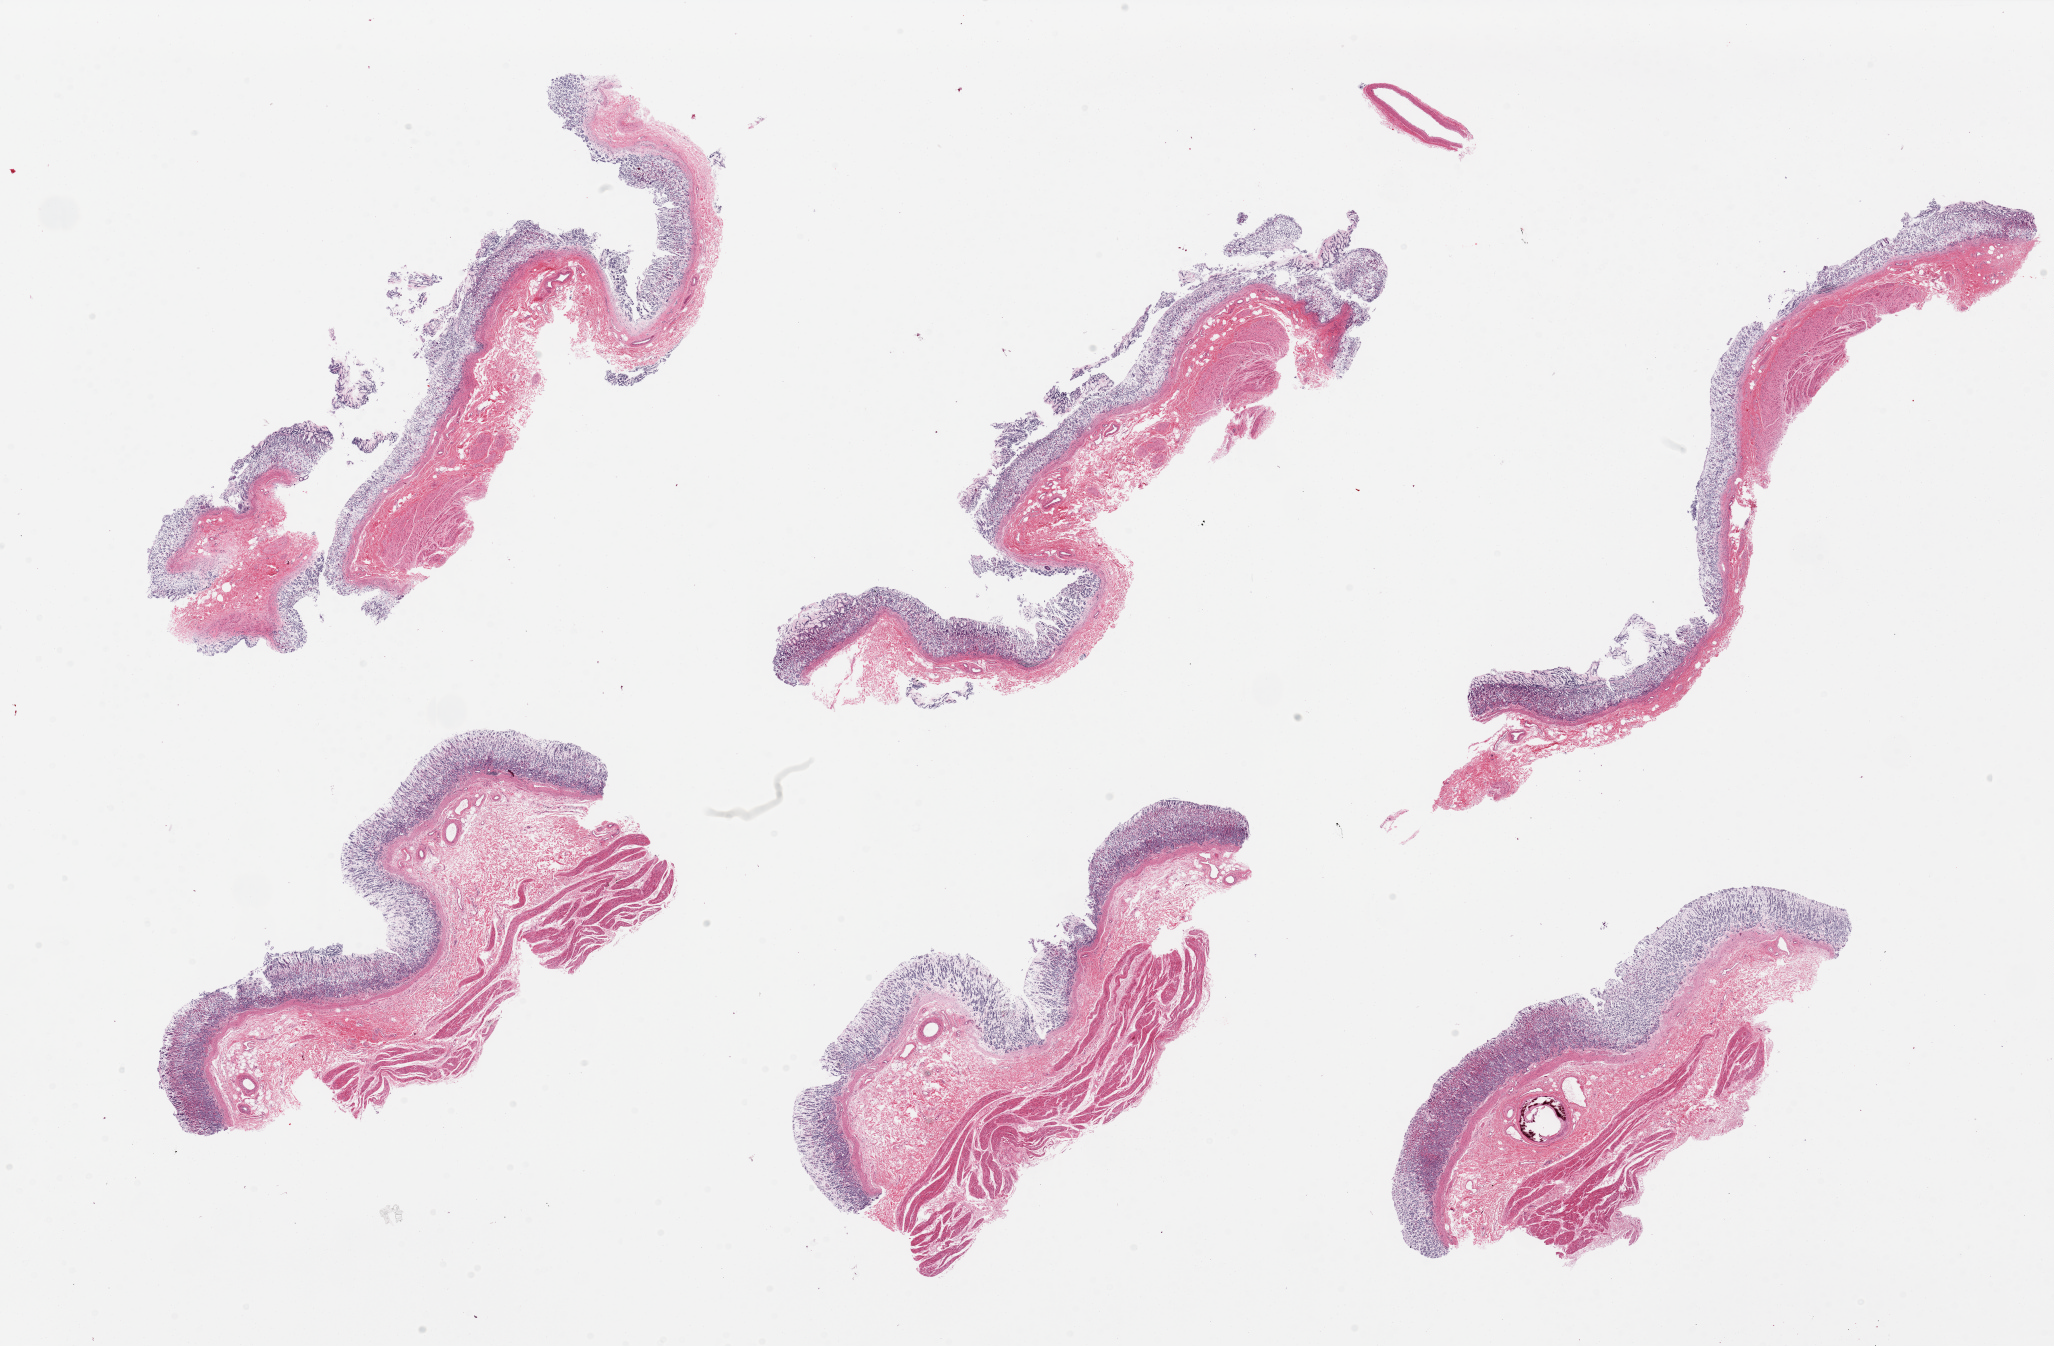
Digitized haematoxylin and eosin-stained section, brightfield — low-resolution overview of the scanned area, about 32.5 x 21.3 mm (slide scanned at 20x); PAXgene-fixed, paraffin-embedded tissue; section of stomach (target tissue); donor tissue sample. Donor: male.
* pathologist's review note for this sample: 6 pieces; only small groups of glands are preserved; of limited value